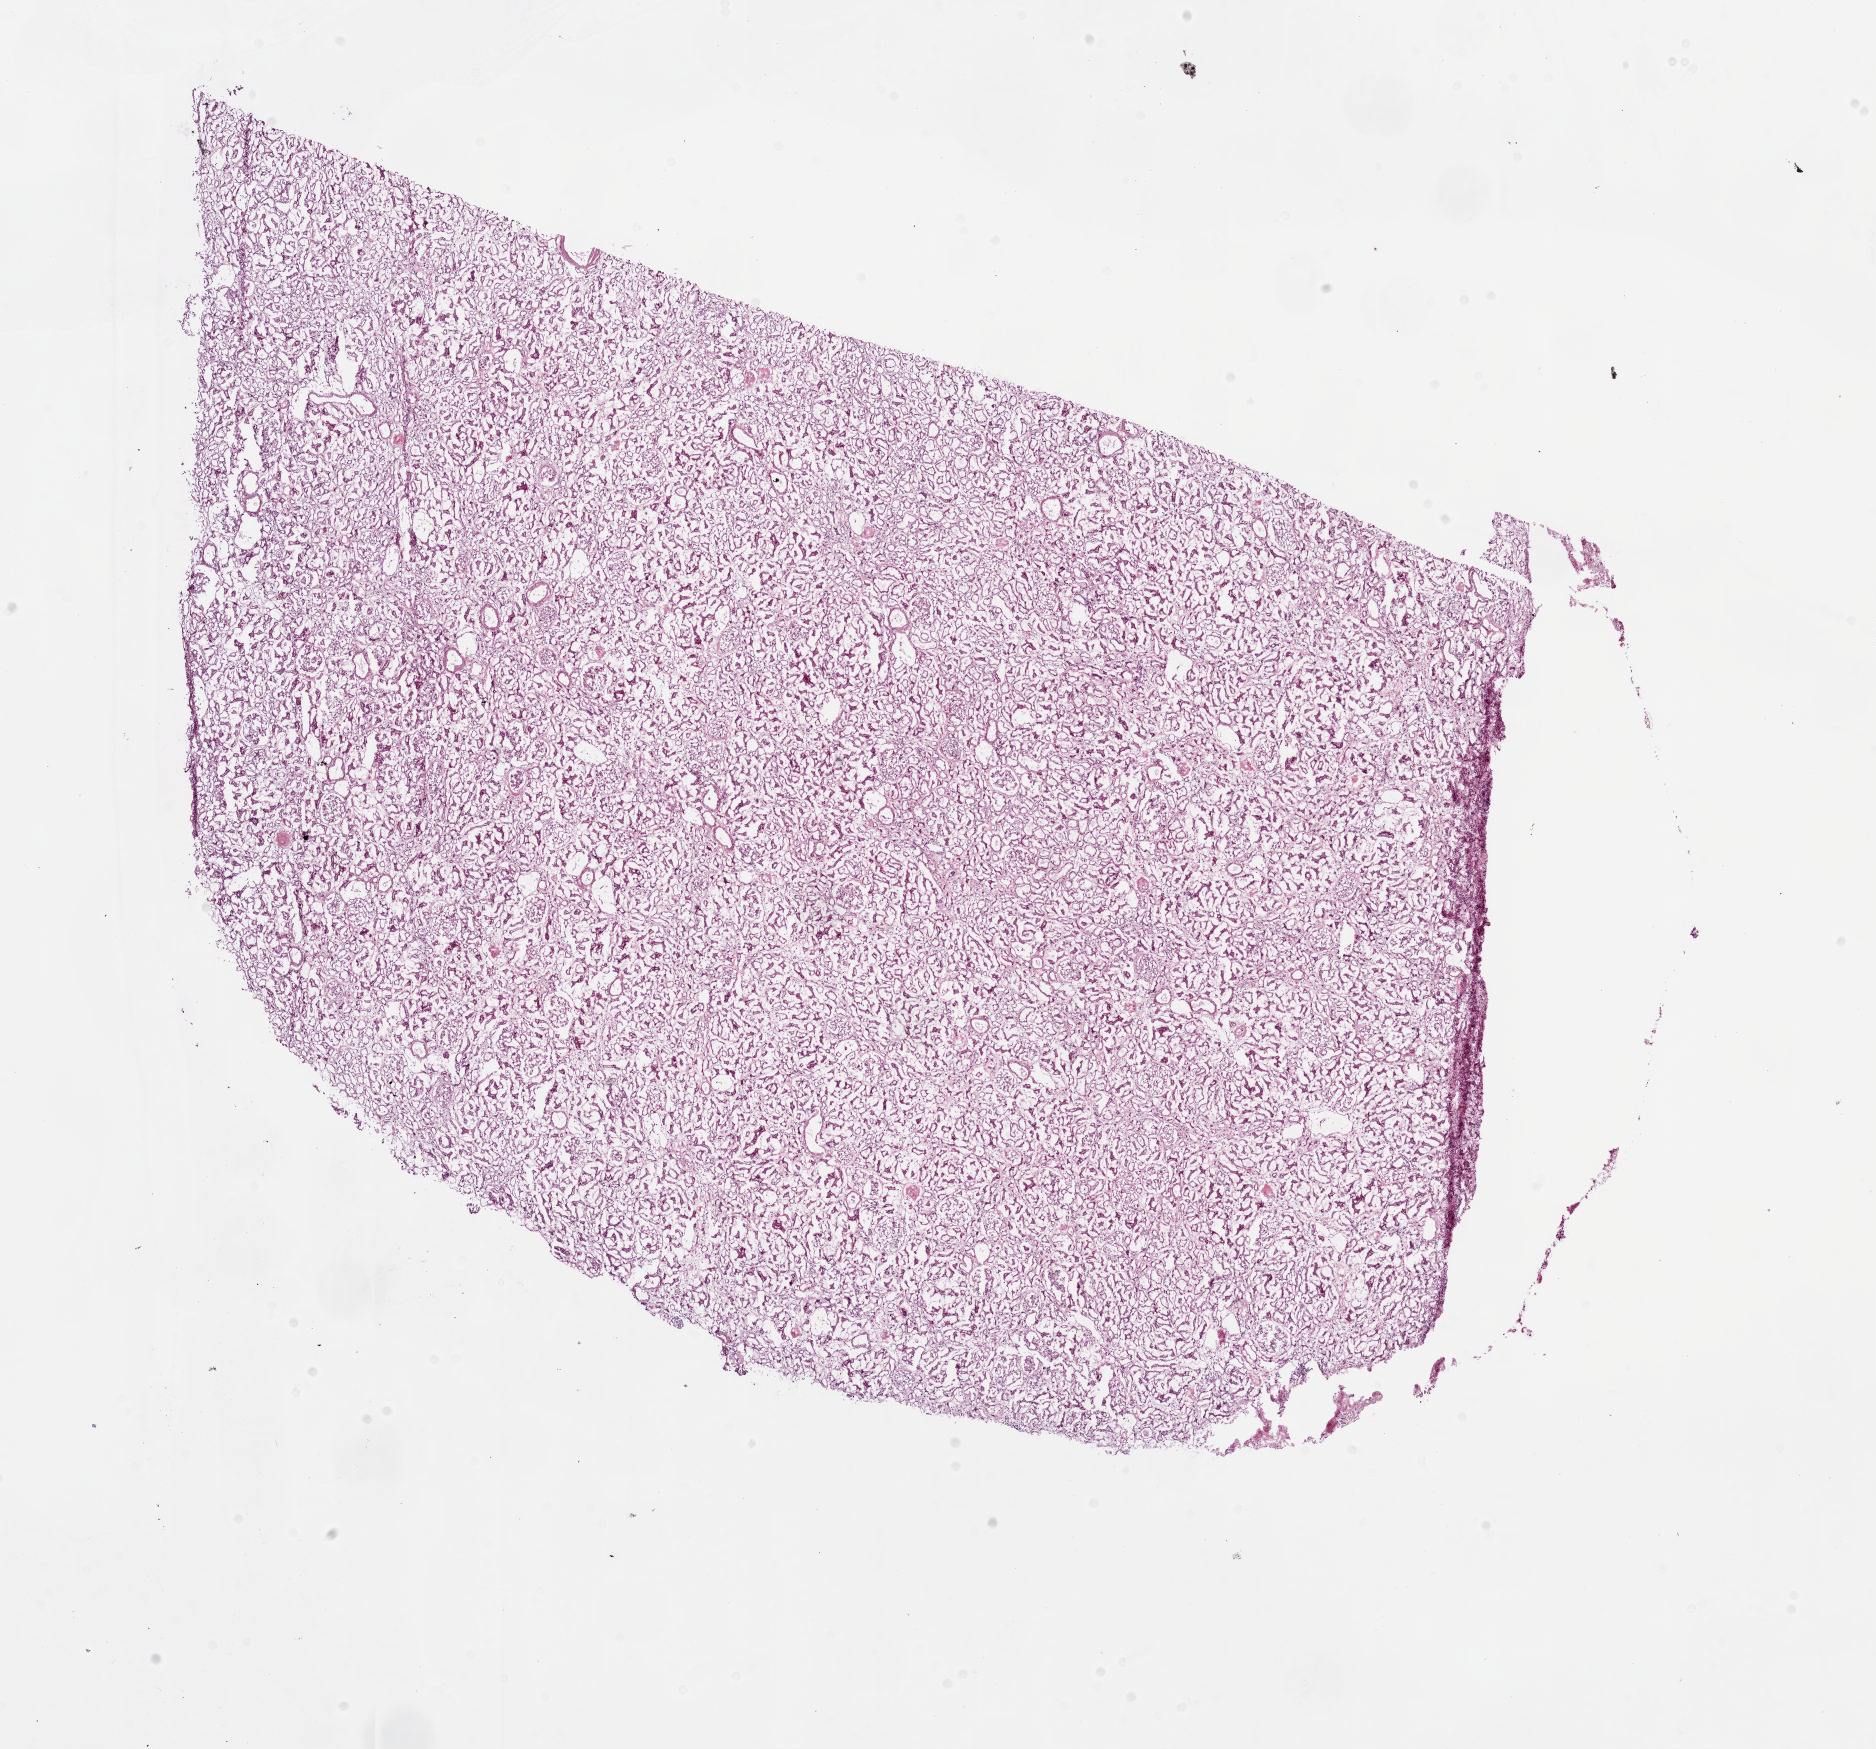
Hematoxylin and eosin (H&E) stained whole-slide image, shown as a low-resolution overview of the whole scanned area (about 14.9 x 13.9 mm), frozen section from the bottom of the tissue portion, sample: solid tissue normal (non-tumour tissue), kidney. Female patient; age at initial diagnosis 76 years.
- this section: solid tissue normal sample (biorepository sample class)
- patient diagnosis: Clear cell adenocarcinoma, NOS